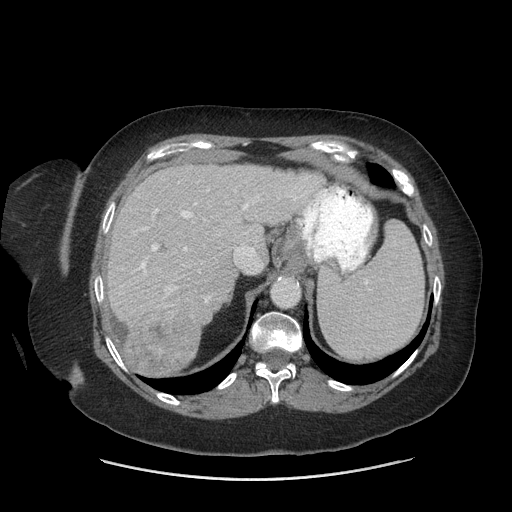
Contrast-enhanced abdominal CT (liver protocol), one axial slice; slice 52 of 69 in the series (ordered by position); reconstruction kernel STANDARD; soft-tissue window (W 400 / L 40 HU); 2.5 mm slice thickness; 512 × 512 image matrix, field of view 420 × 420 mm. Case-level facts recorded for this patient, not image findings: diagnosis: hepatocellular carcinoma (patient treated with transarterial chemoembolisation; whether this scan precedes or follows treatment is not stated here); TNM stage (as recorded): Stage-IIIB; Child-Pugh class: A; tumour differentiation: moderately differentiated.
Annotated regions visible in this slice (semi-automatic segmentation, software-assisted and operator-edited):
- liver parenchyma outside the tumour (the mass and vessels are separate outlines, so this box may not span the whole liver): bounding box [x1, y1, x2, y2] px = [105, 164, 320, 374]
- mass: [122, 306, 200, 375]
- liver vessels: [121, 187, 307, 302]